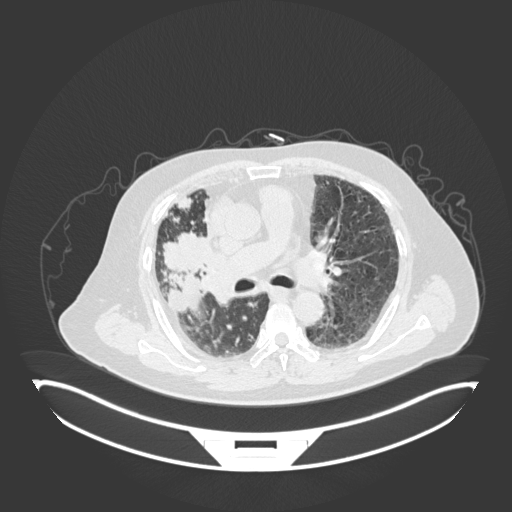
Chest CT, one axial slice. Position 98 of 201 along the scan axis. 120 kVp. Lung window (W 1500 / L -600 HU). 1 mm slice thickness. 512 × 512 image matrix, field of view 500 × 500 mm. Patient: male, 69 years. From the clinical record (not read from this slice): clinical TNM (as recorded): T4 N3 M1.
Annotated regions visible in this slice (rectangle marked by the reading radiologist):
- lung tumour (recorded histology: adenocarcinoma): bounding box <160,228,216,278> (left, top, right, bottom; pixels)